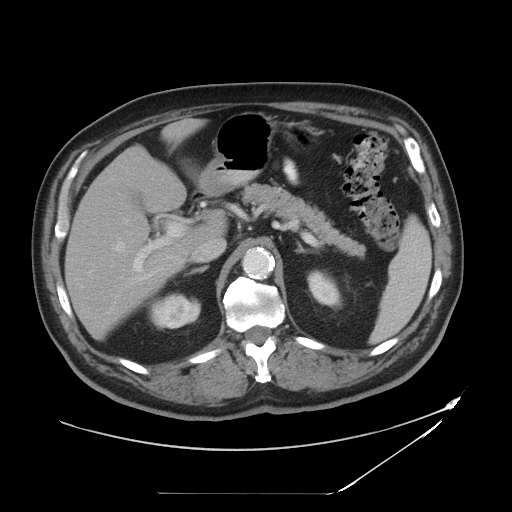
Contrast-enhanced abdominal CT, one axial slice; position 27 of 49 along the scan axis; soft-tissue window (W 400 / L 40 HU); 512 × 512 image matrix, field of view 461 × 461 mm. Male patient, age 72 years. From the clinical record (not read from this slice): diagnosis: colorectal cancer liver metastases, imaged before liver resection; multiple liver metastases: no; largest metastasis: 2.5 cm; chemotherapy before resection: yes.
Structures marked on this image (manually delineated by an expert):
- hepatic veins: bounding box (x1, y1, x2, y2) in pixels: (87, 238, 126, 275)
- liver: (65, 124, 219, 336)
- planned liver remnant (the part of the liver to remain after resection): (65, 165, 188, 336)
- portal vein (with intrahepatic branches): (131, 219, 189, 283)